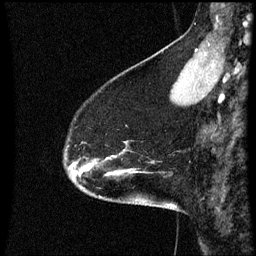
Breast MRI (dynamic contrast-enhanced), one sagittal slice. Position 12 of 60 along the scan axis. Dynamic contrast-enhanced series, image 2 of 3 at this slice position (ordered by acquisition). 1.5 T. TE 4.2 ms, TR 8.9 ms. 2 mm slice thickness. 256 × 256 image matrix, field of view 200 × 200 mm. Female patient, age 45 years. From the clinical record (not read from this slice): setting: breast cancer imaged before/during neoadjuvant chemotherapy; receptor status: HR-positive, HER2-negative.
Structures marked on this image (semi-automatic segmentation, software-assisted and operator-edited):
- analysis volume of interest (the breast-tissue region the enhancement analysis was run in; not a lesion): bounding box (x1, y1, x2, y2) in pixels: (66, 142, 171, 205)
- tumour enhancement mask (voxels above the 70 % enhancement threshold inside the analysis volume of interest): (74, 168, 89, 177)